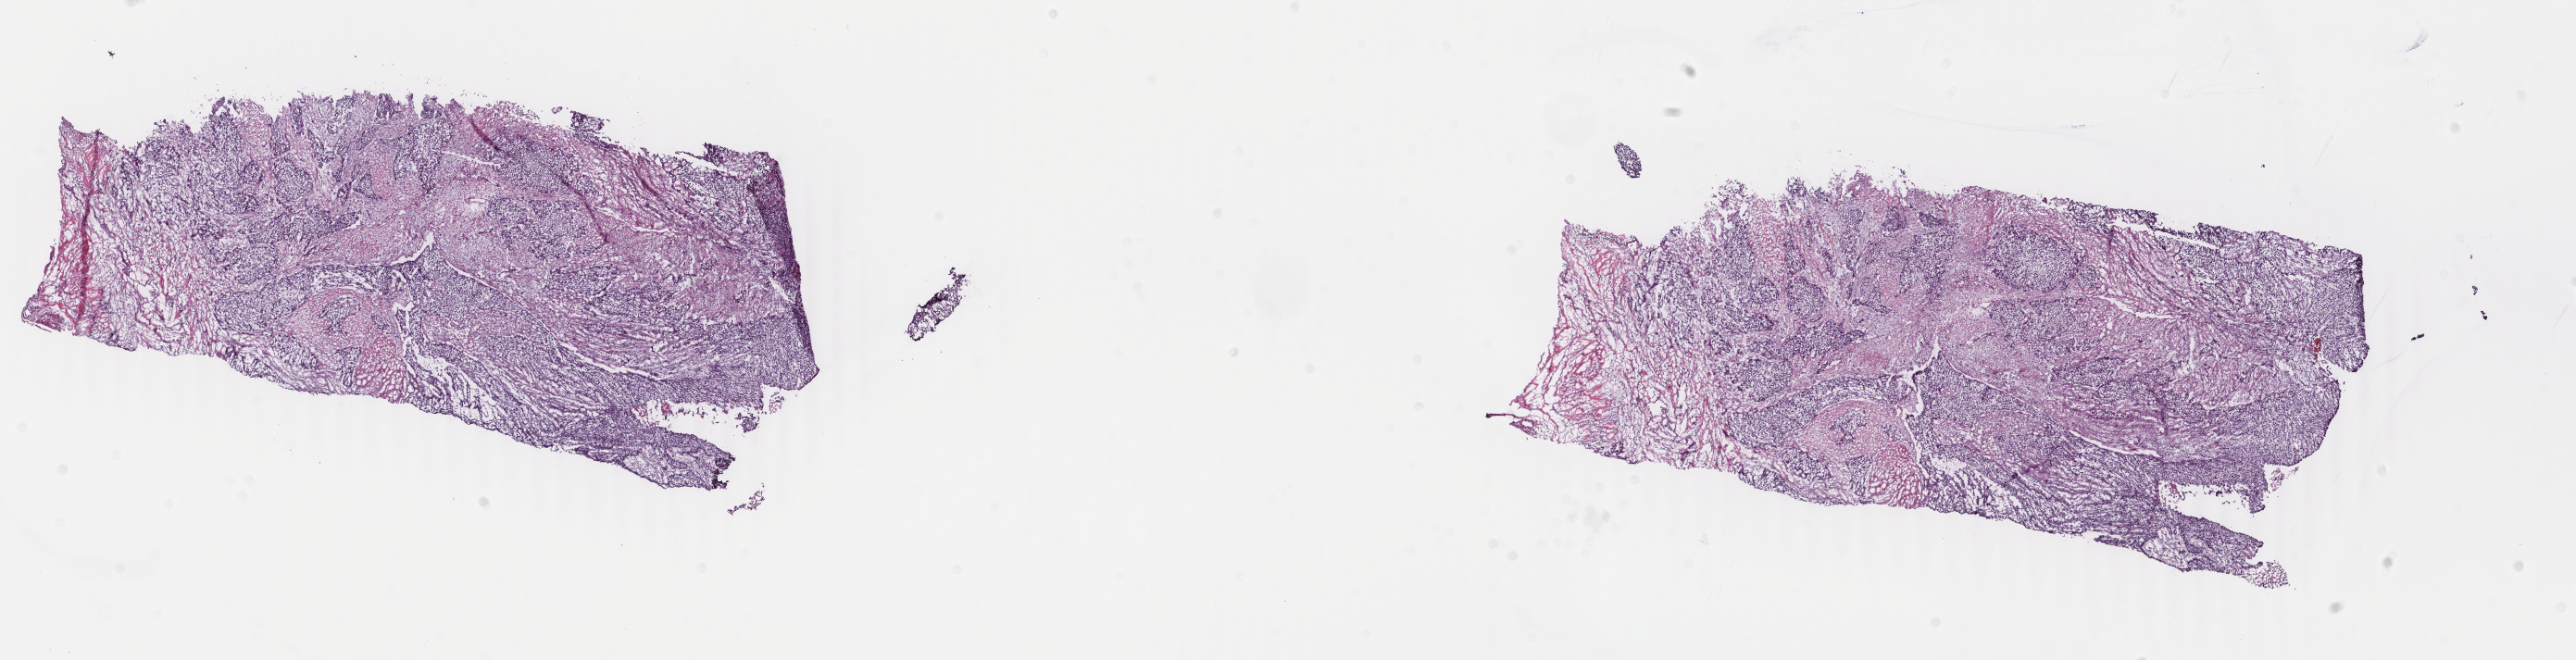
H&E-stained whole-slide image, a low-resolution overview of the entire scanned area, about 22.1 x 5.7 mm (acquisition: 40x scan), frozen section from the top of the tissue portion, bladder, primary tumour sample. Patient: male, age at initial diagnosis 79 years. Histologic grade: high grade. Composition of this section per pathologist review: tumour cells 70%, tumour nuclei 70%, normal cells 0%, stromal cells 30%, necrosis 0%. Inflammatory infiltration, as recorded: lymphocyte infiltration 5%, monocyte infiltration 0%, neutrophil infiltration 0%.
- histologic diagnosis: Transitional cell carcinoma
- AJCC pathologic stage: II (6th edition)
- lymph nodes positive (case pathology): 0 of 27 examined